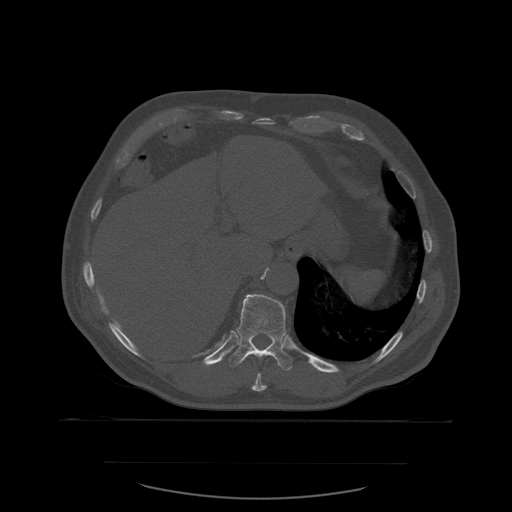
CT including the spine, one axial slice. Position 301 of 590 along the scan axis. Bone window (W 1800 / L 400 HU). 1.25 mm slice thickness. 512 × 512 image matrix. Patient age 71 years. Case-level facts recorded for this patient, not image findings: primary cancer: lung; vertebrae with lytic lesions (as recorded): T1, T2, L5, S1.
Annotated regions visible in this slice (semi-automatically segmented with operator editing):
- T10 vertebra: bounding box (x1, y1, x2, y2) in pixels: (252, 373, 267, 392)
- T11 vertebra: (229, 294, 294, 371)